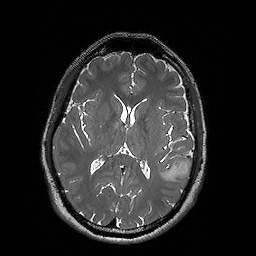
Brain MRI from a brain-tumour surgery series, one axial slice. Position 83 of 192 along the scan axis. 1 mm slice thickness. 256 × 256 image matrix, field of view 250 × 250 mm. From the clinical record (not read from this slice): histopathology: Oligodendroglioma; WHO grade: 2; IDH mutation: yes.
Annotated regions visible in this slice (manually delineated by an expert):
- tumour: box from (x=159, y=160) to (x=193, y=181) px